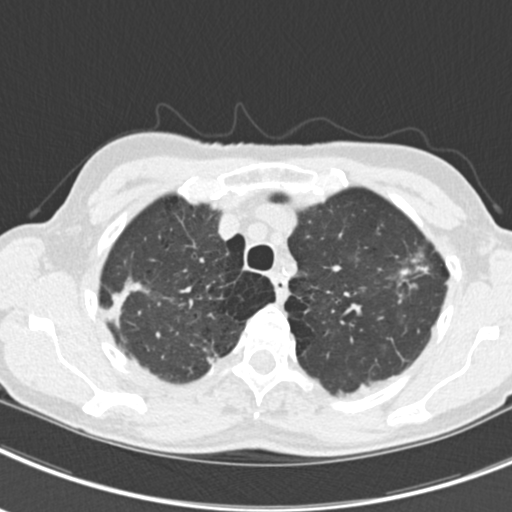
Chest CT (low-dose screening protocol), one axial image; second screening round (one year after baseline); lung window (W 1500 / L -600 HU); 2 mm slice thickness; standard (soft-tissue) reconstruction kernel (B30f); 512 × 512 image matrix. Female, age 63 years at enrolment. Current smoker at enrolment.
Expert reader's lesion annotation, bounding box (x1, y1, x2, y2) in pixels: (385, 238, 451, 300). The screening reader recorded 9 non-calcified nodules or masses ≥4 mm on this exam; which of them this box marks is not recorded. Official screen result: positive, other. Later outcome: lung cancer diagnosed 408 days after this screen (after the third annual screen) — bronchiolo-alveolar adenocarcinoma, NOS, right upper lobe, right middle lobe, right lower lobe, left upper lobe, left lower lobe, moderately differentiated (G2), stage IV (AJCC 6th edition).